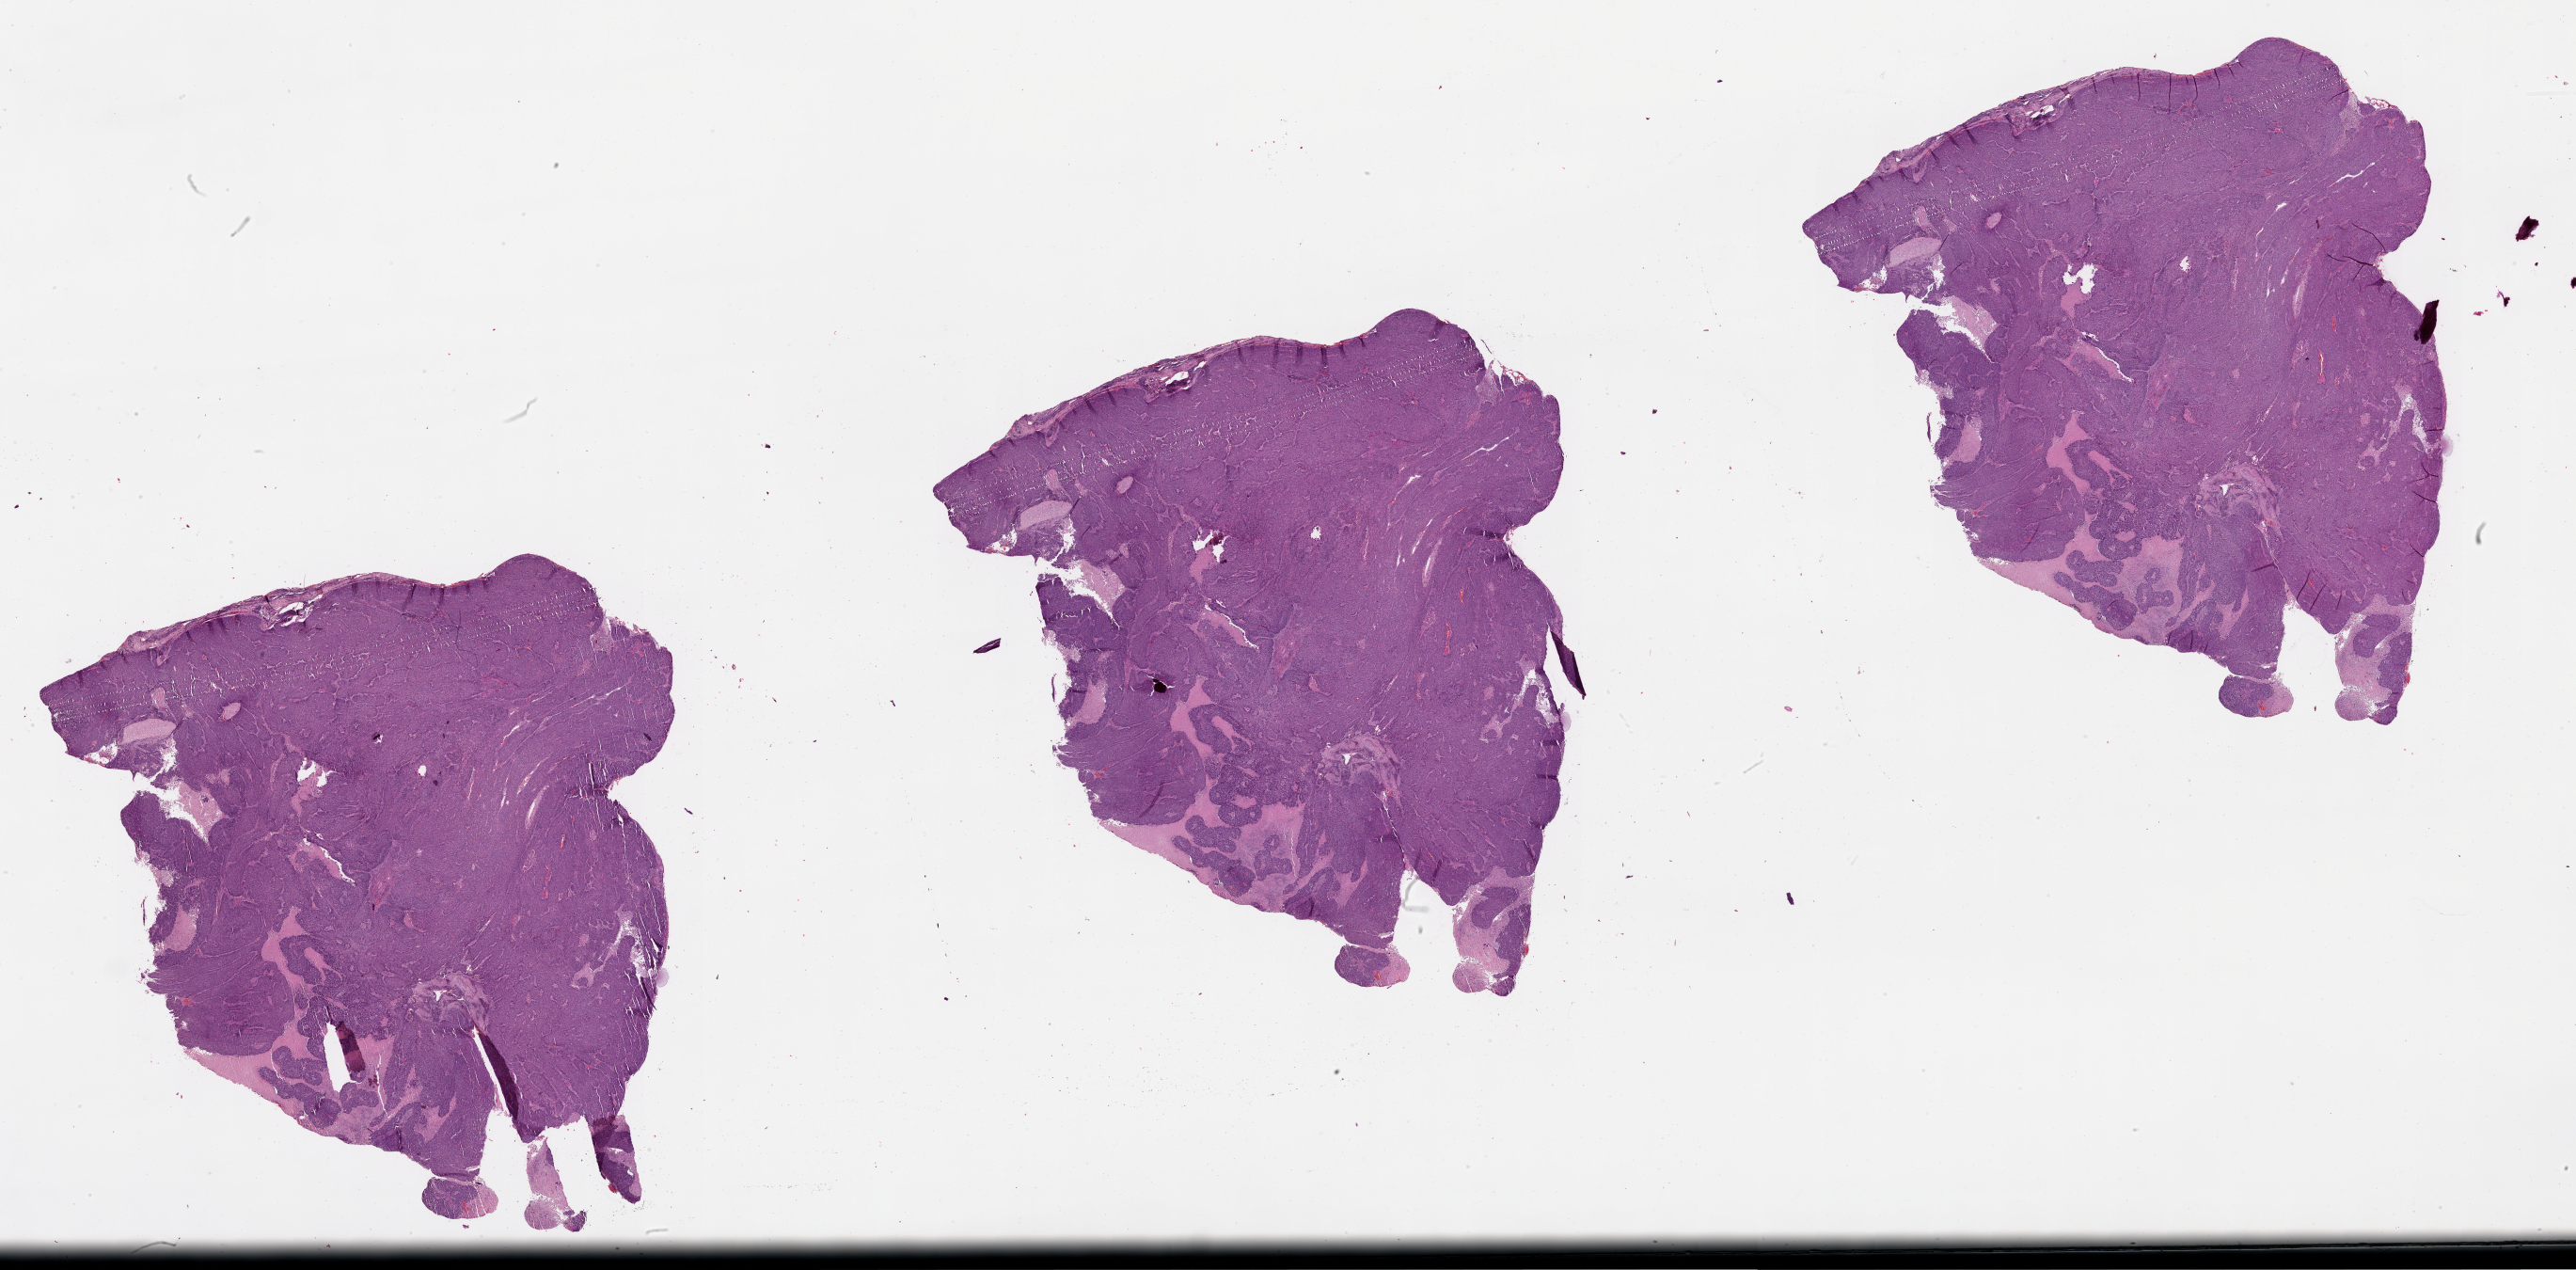
Digitized Hematoxylin and eosin (H&E) stained tissue section (whole slide), low-resolution overview of the scanned area, about 44.1 x 21.7 mm. Tumour tissue sample, lung. 58-year-old male patient.
Patient diagnosis (cohort enrolment): squamous cell carcinoma (lung).